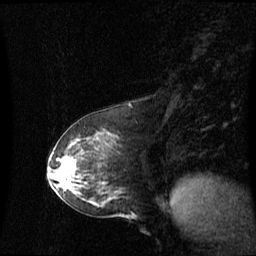
Breast MRI (dynamic contrast-enhanced), one sagittal slice; position 28 of 60 along the scan axis; dynamic contrast-enhanced series, image 2 of 3 at this slice position (ordered by acquisition); 1.5 T; TE 4.2 ms, TR 8.4 ms; 2.1 mm slice thickness; 256 × 256 image matrix. Patient: female, 59 years. From the clinical record (not read from this slice): setting: breast cancer imaged before/during neoadjuvant chemotherapy; receptor status: HR-positive, HER2-negative.
Annotated regions visible in this slice (semi-automatically segmented with operator editing):
- analysis volume of interest (the breast-tissue region the enhancement analysis was run in; not a lesion): bounding box [x1, y1, x2, y2] px = [55, 148, 87, 191]
- tumour enhancement mask (voxels above the 70 % enhancement threshold inside the analysis volume of interest): [64, 160, 76, 171]